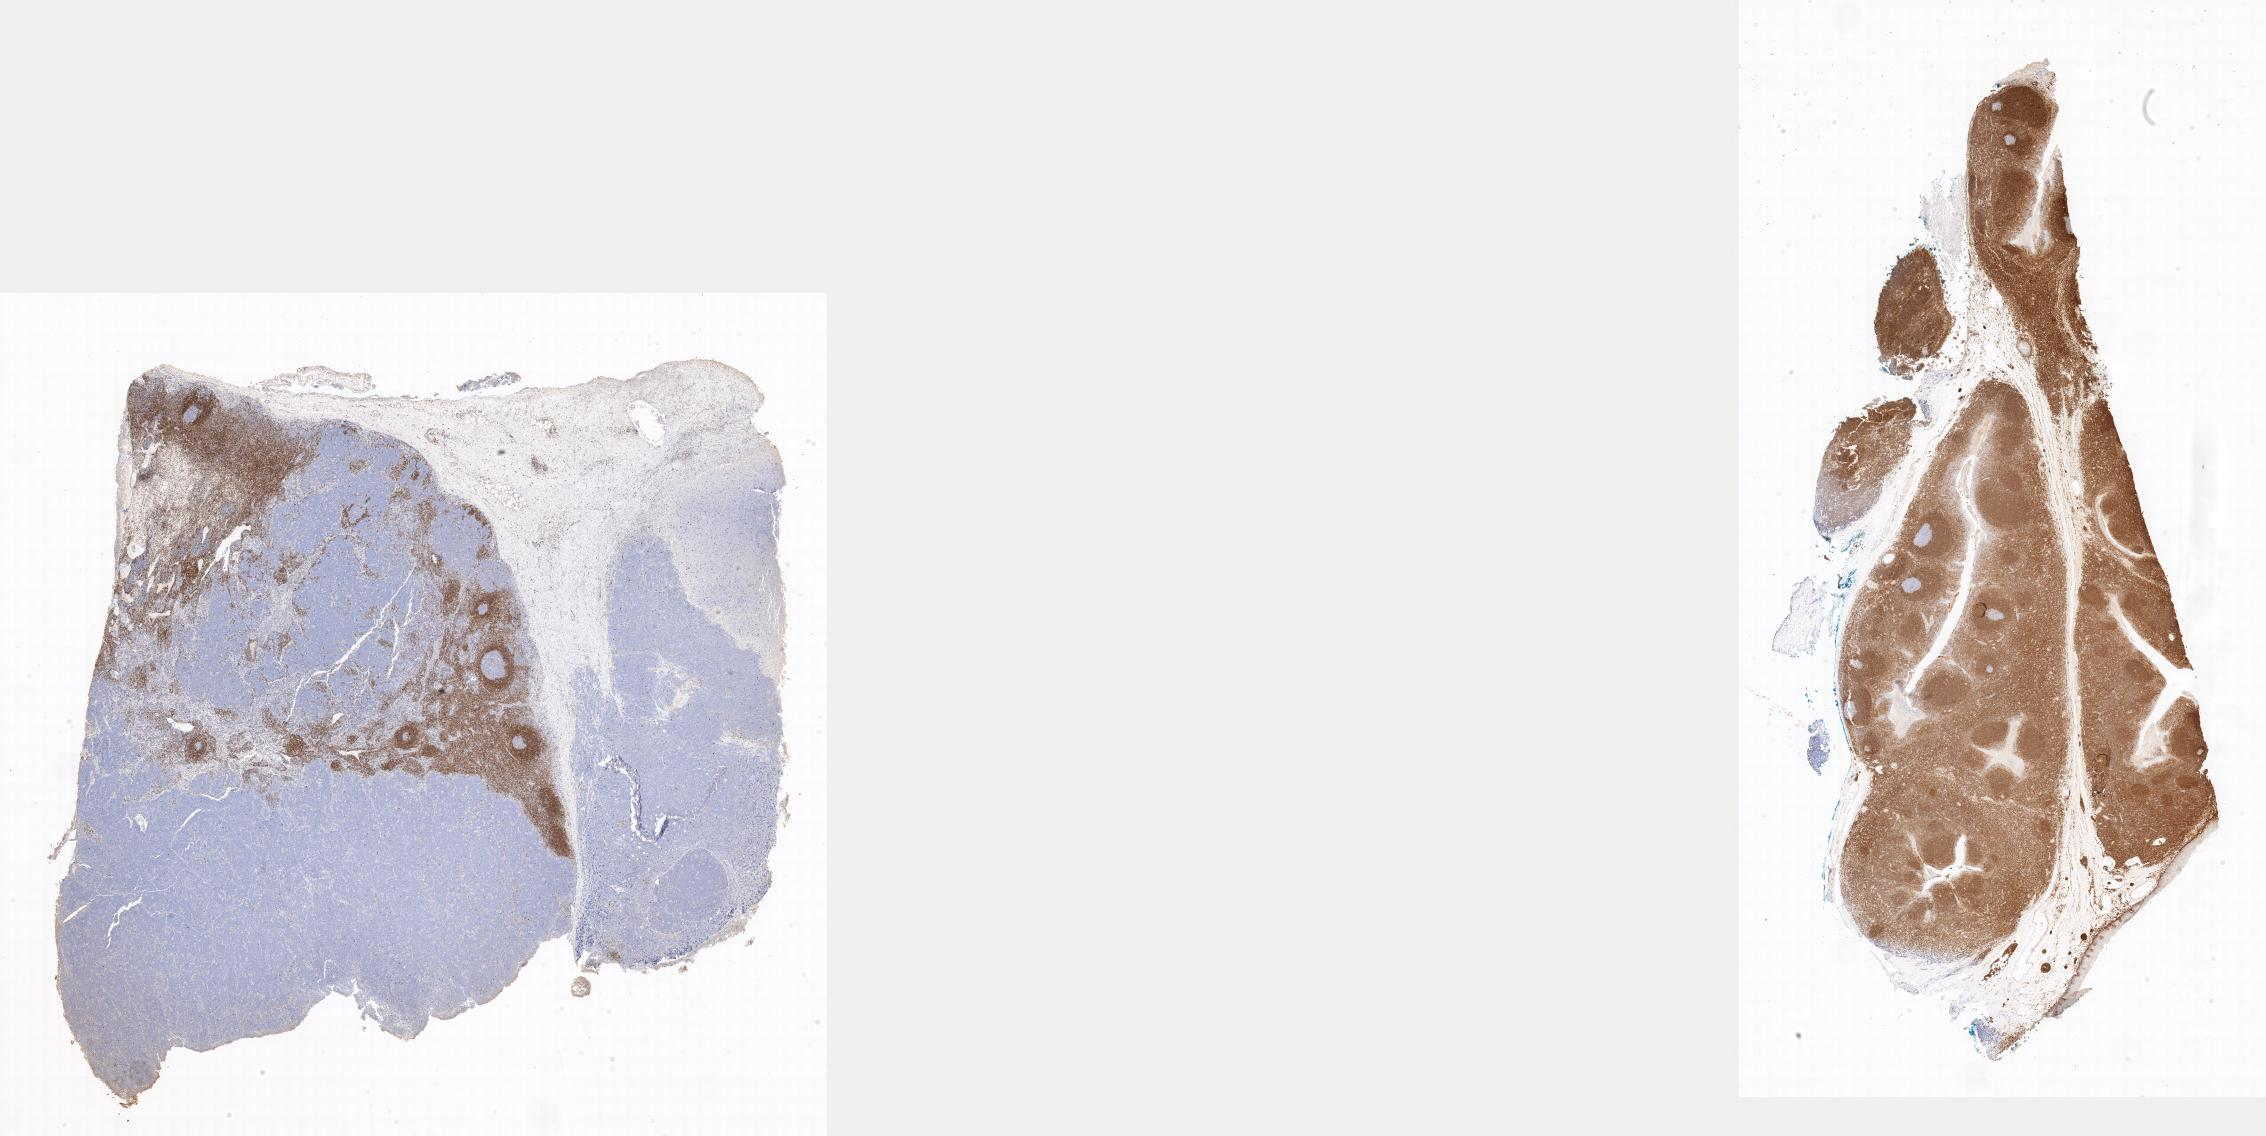
Whole-slide image, immunohistochemical stain for BCL2, a low-resolution overview of the entire scanned area, specimen: tumor tissue, site: abdominal lymph node. Patient female; age 14 years.
Histologic diagnosis: Burkitt lymphoma, NOS.